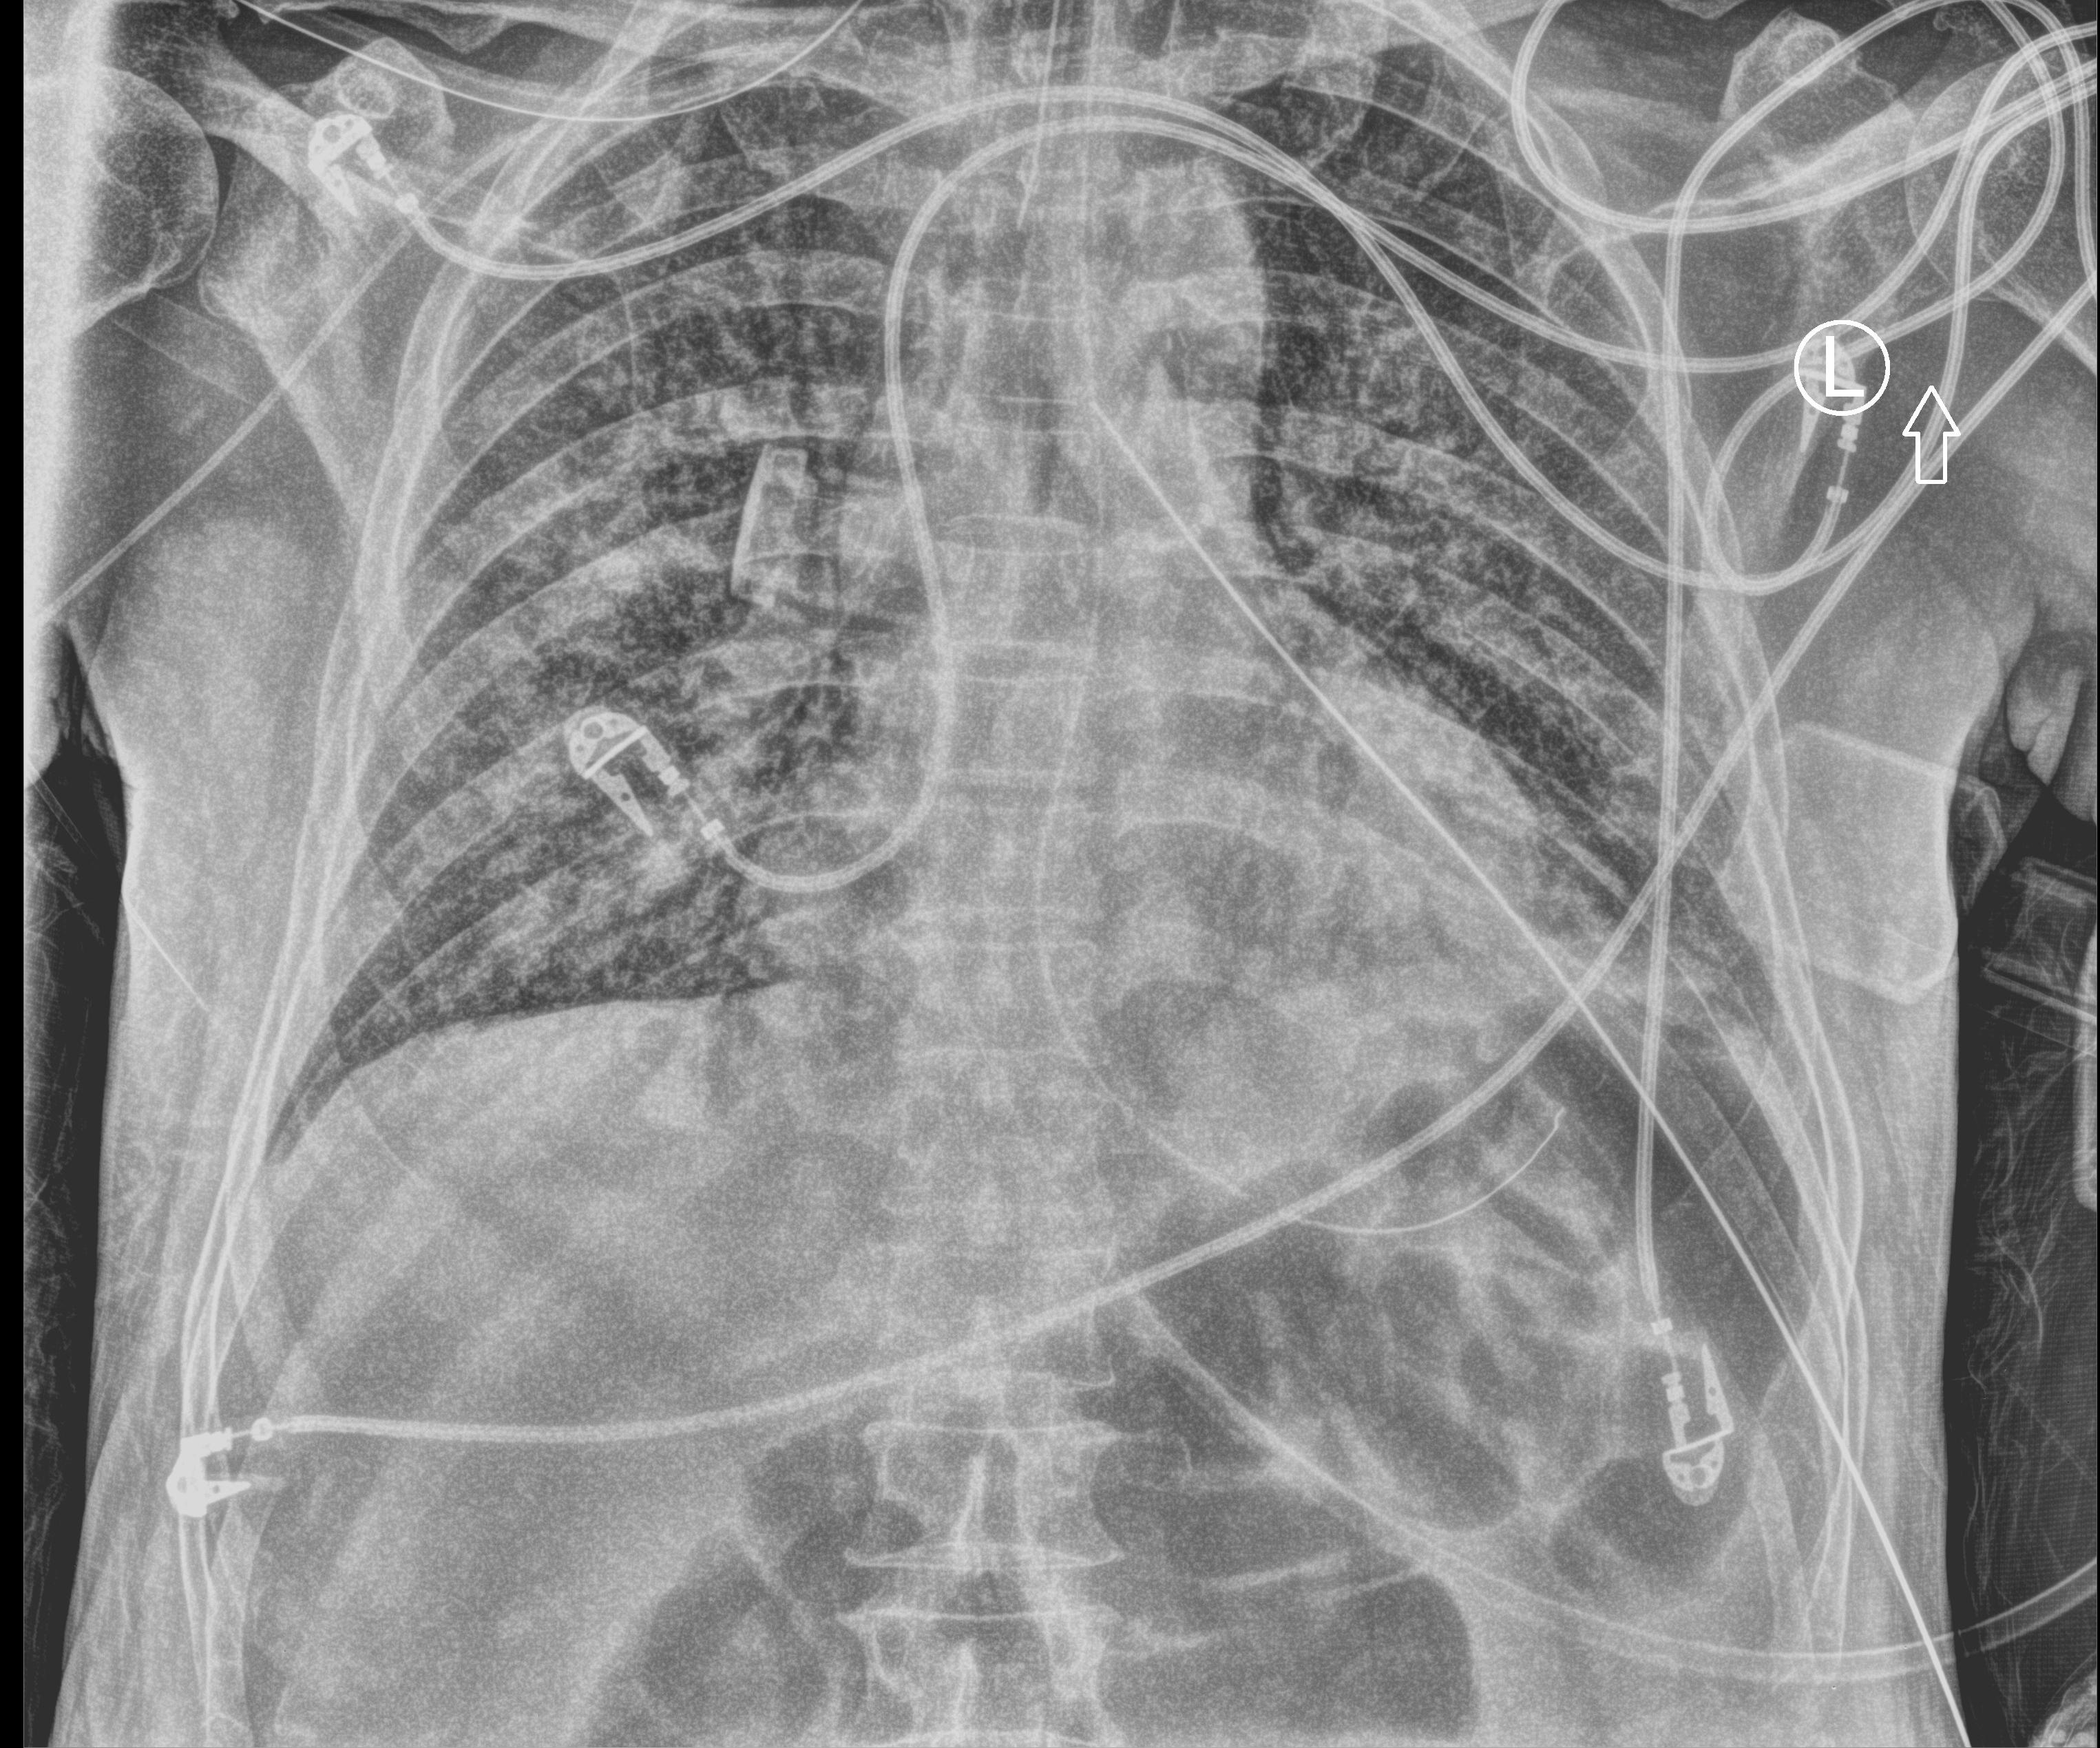
Bedside chest radiograph (computed radiography), anteroposterior (AP) projection. Patient hospitalised with COVID-19; male, aged 60–74 years.
From the hospital-stay record, not from the radiograph (when in the stay this image was taken is not recorded):
- admitted to intensive care during this hospital stay: yes
- length of hospital stay: 37 days